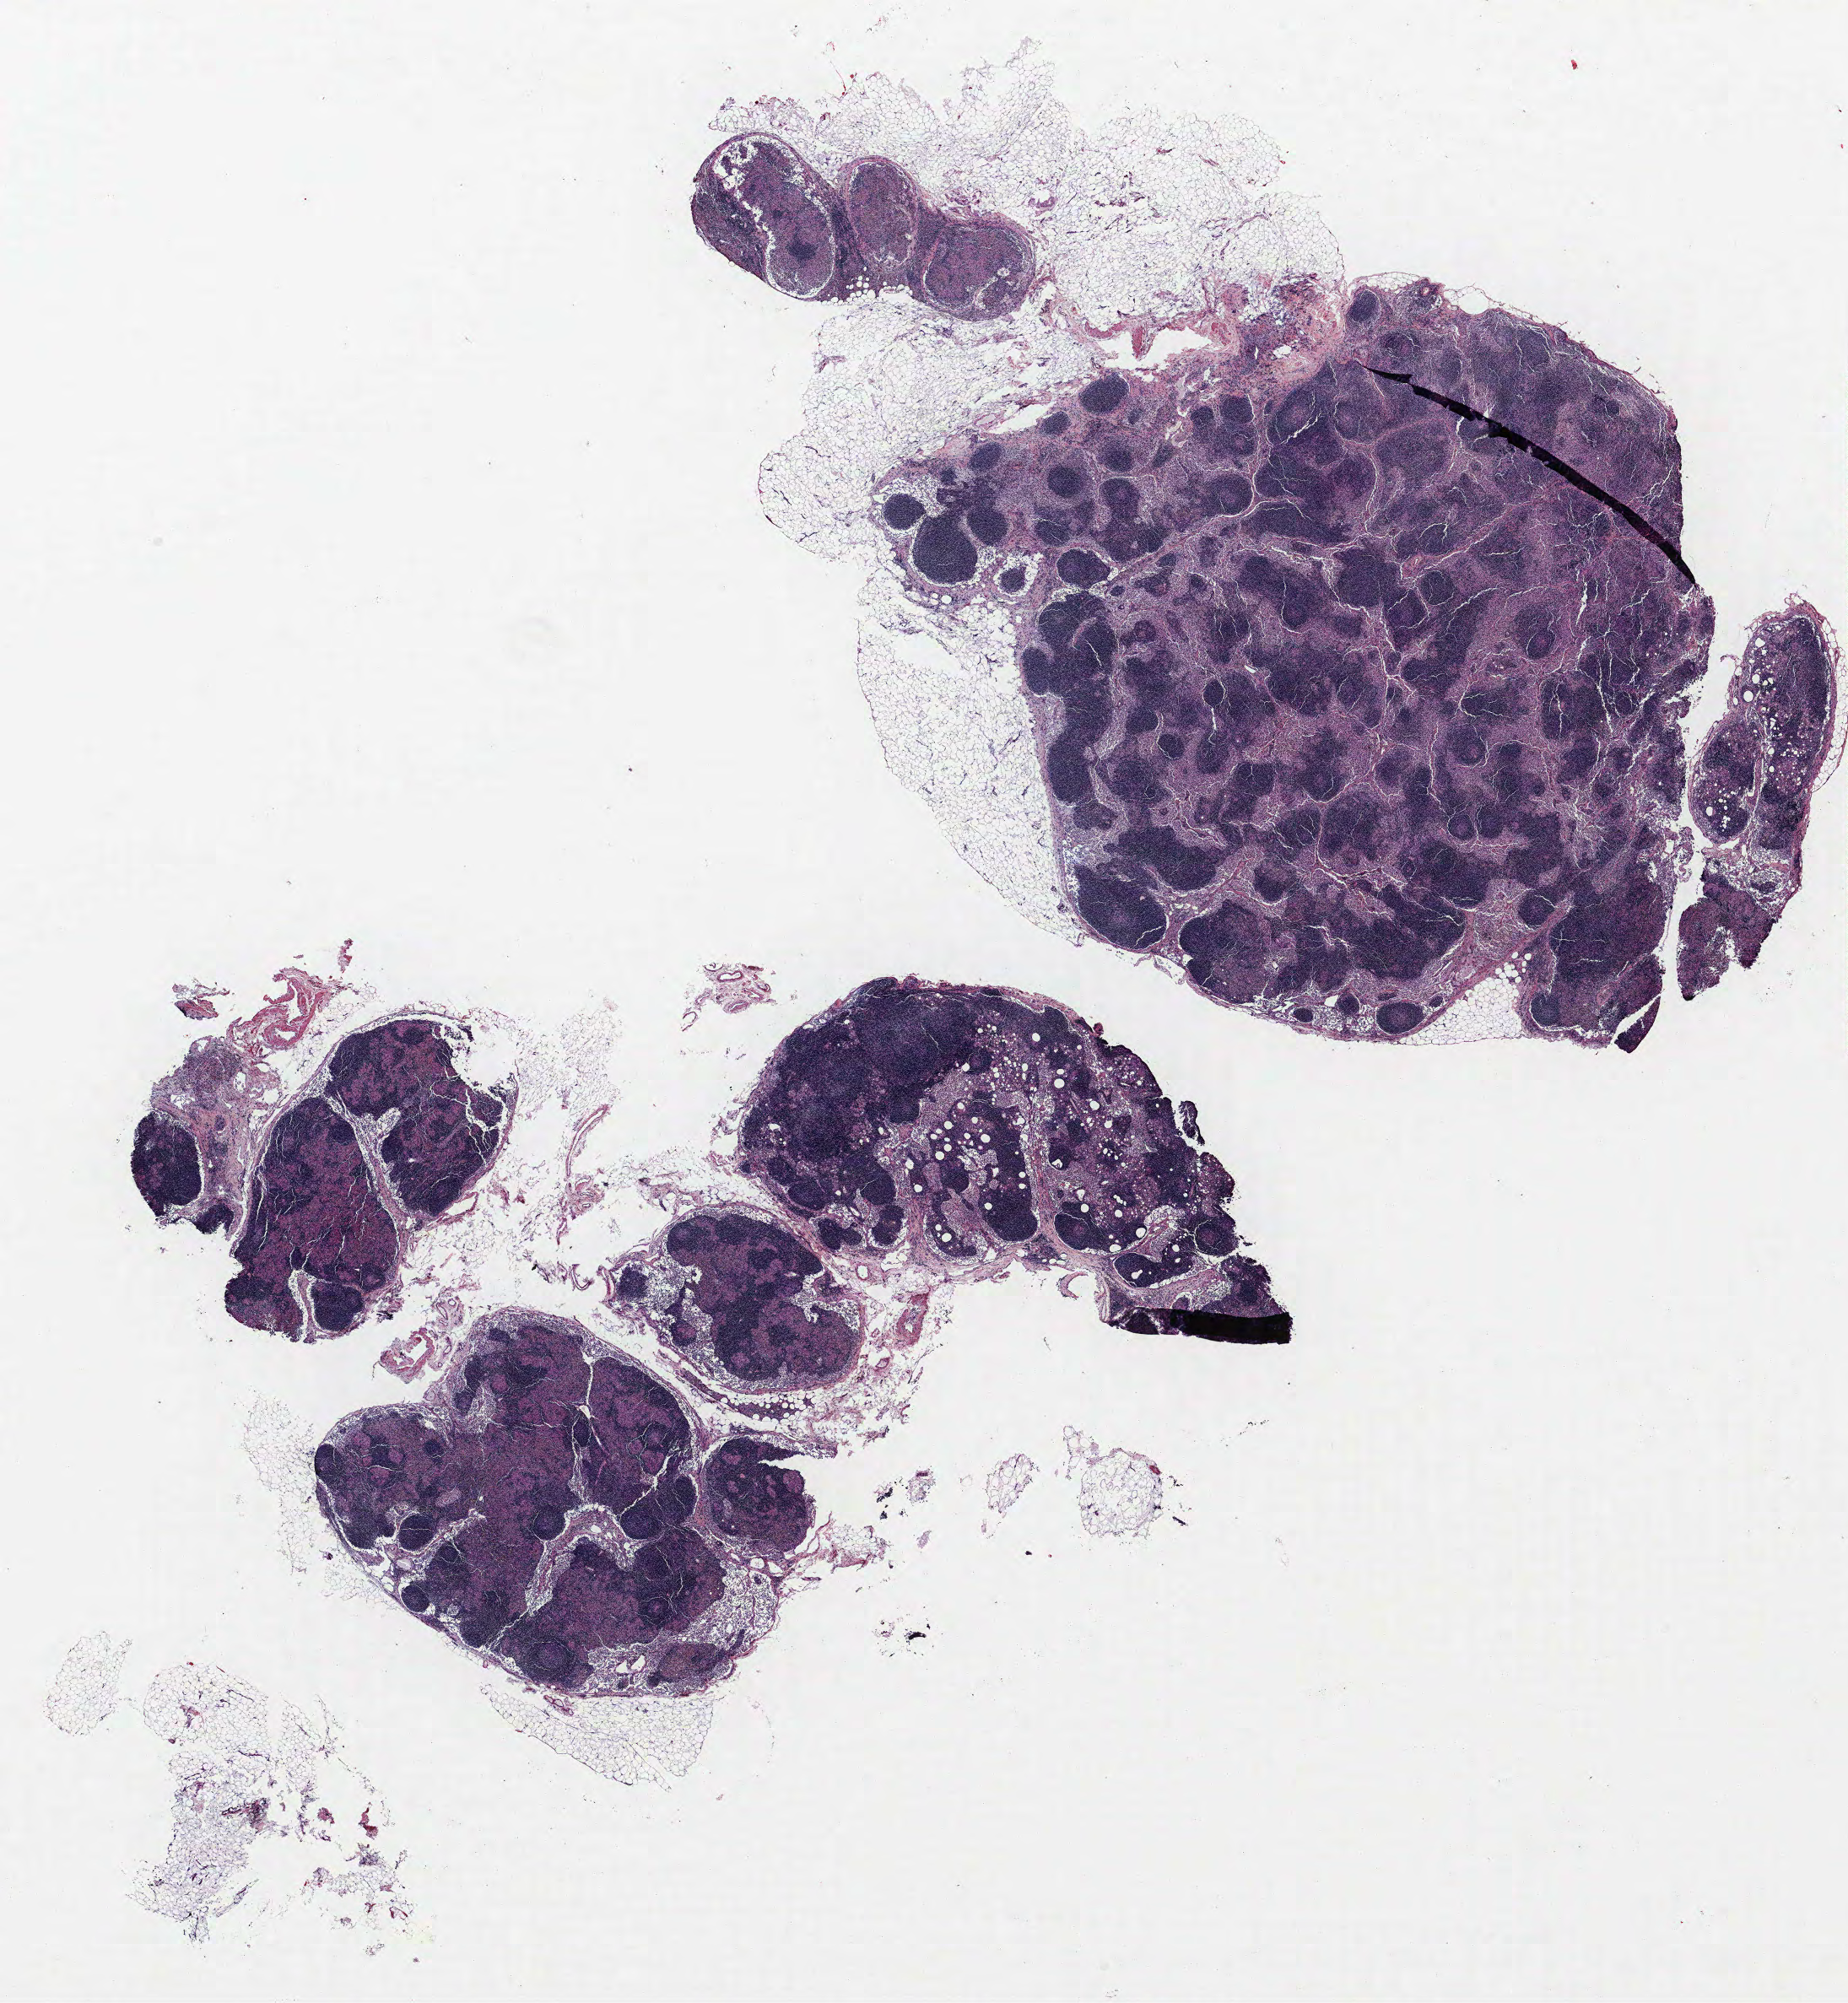
H&E-stained whole-slide image, shown as a low-resolution overview of the whole scanned area (about 17.5 x 19.0 mm); formalin-fixed paraffin-embedded (FFPE) section; lung tissue. Female patient, aged 63 at enrolment. Current smoker at enrolment. Grade: moderately differentiated (G2).
* tumour size (pathology): 28 mm
* primary tumour location (clinical record): right lower lobe
* participant's lung-cancer diagnosis: Mucinous adenocarcinoma
* stage (AJCC 6th edition): IIA